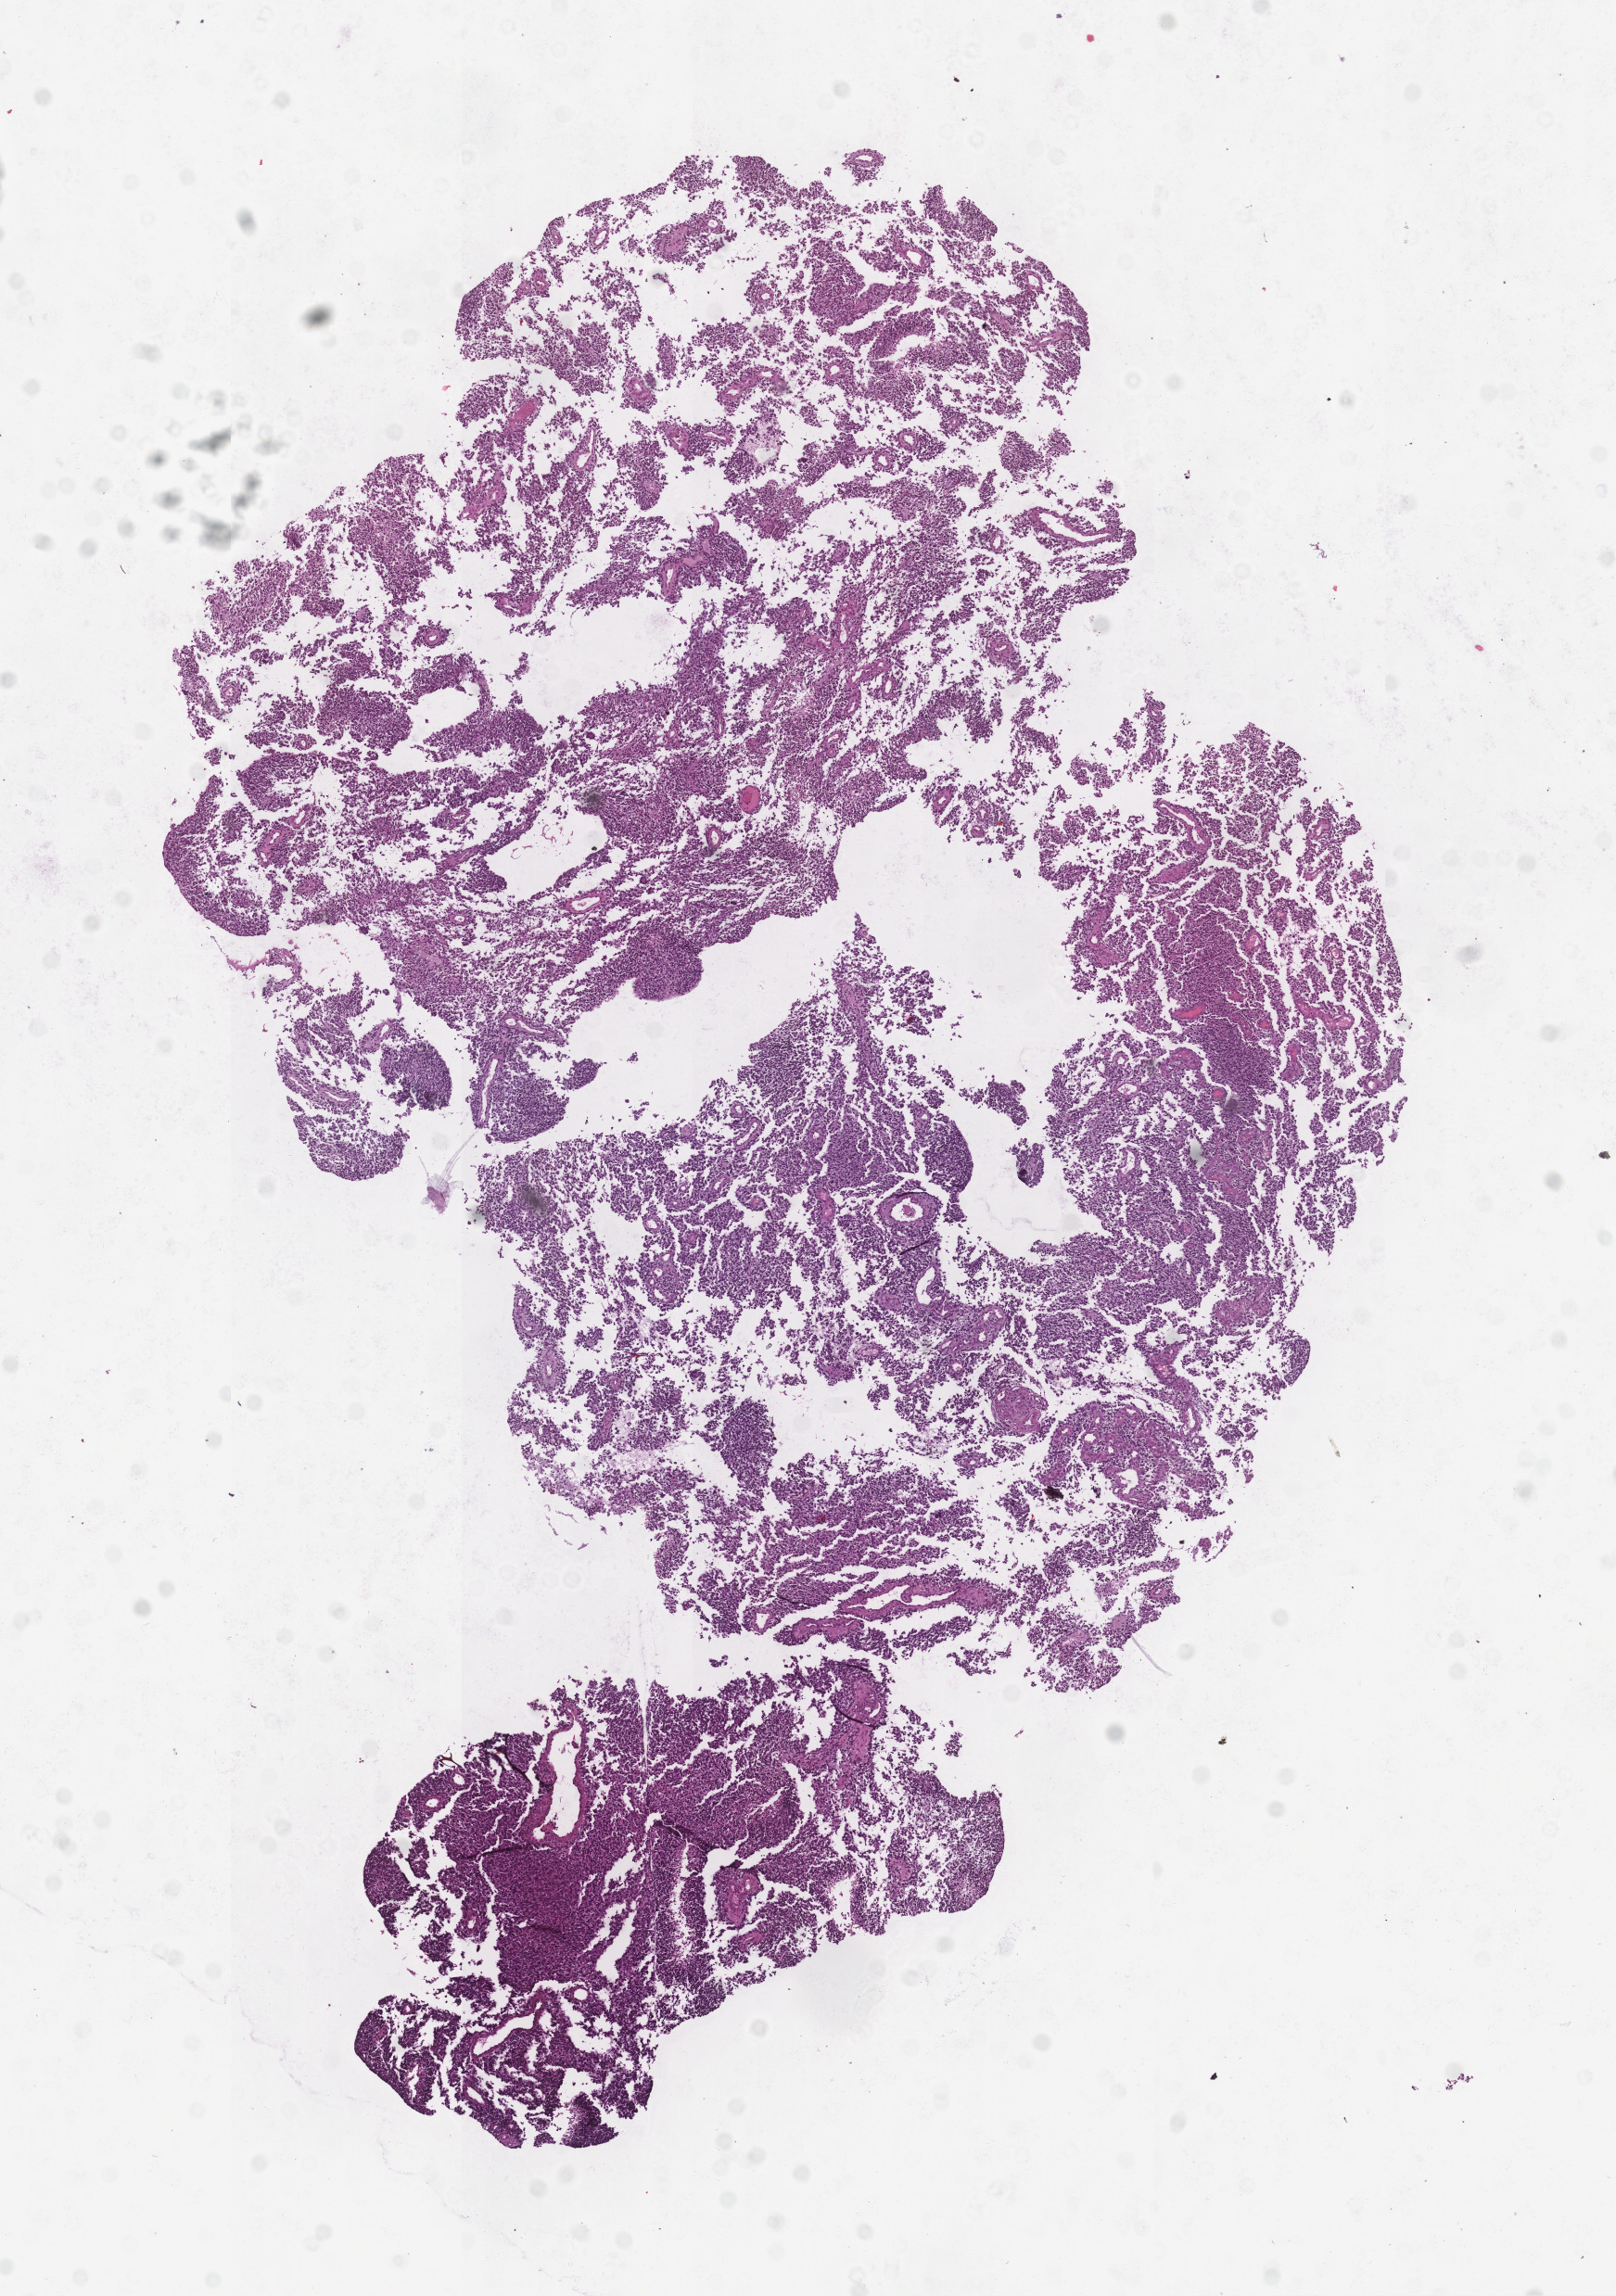
Whole-slide histology image, H&E, low-resolution overview of the scanned area, about 7.0 x 10.0 mm (from a 20x scan). Brain, tumour tissue. 29-year-old female patient.
Histologic diagnosis: Glioblastoma.